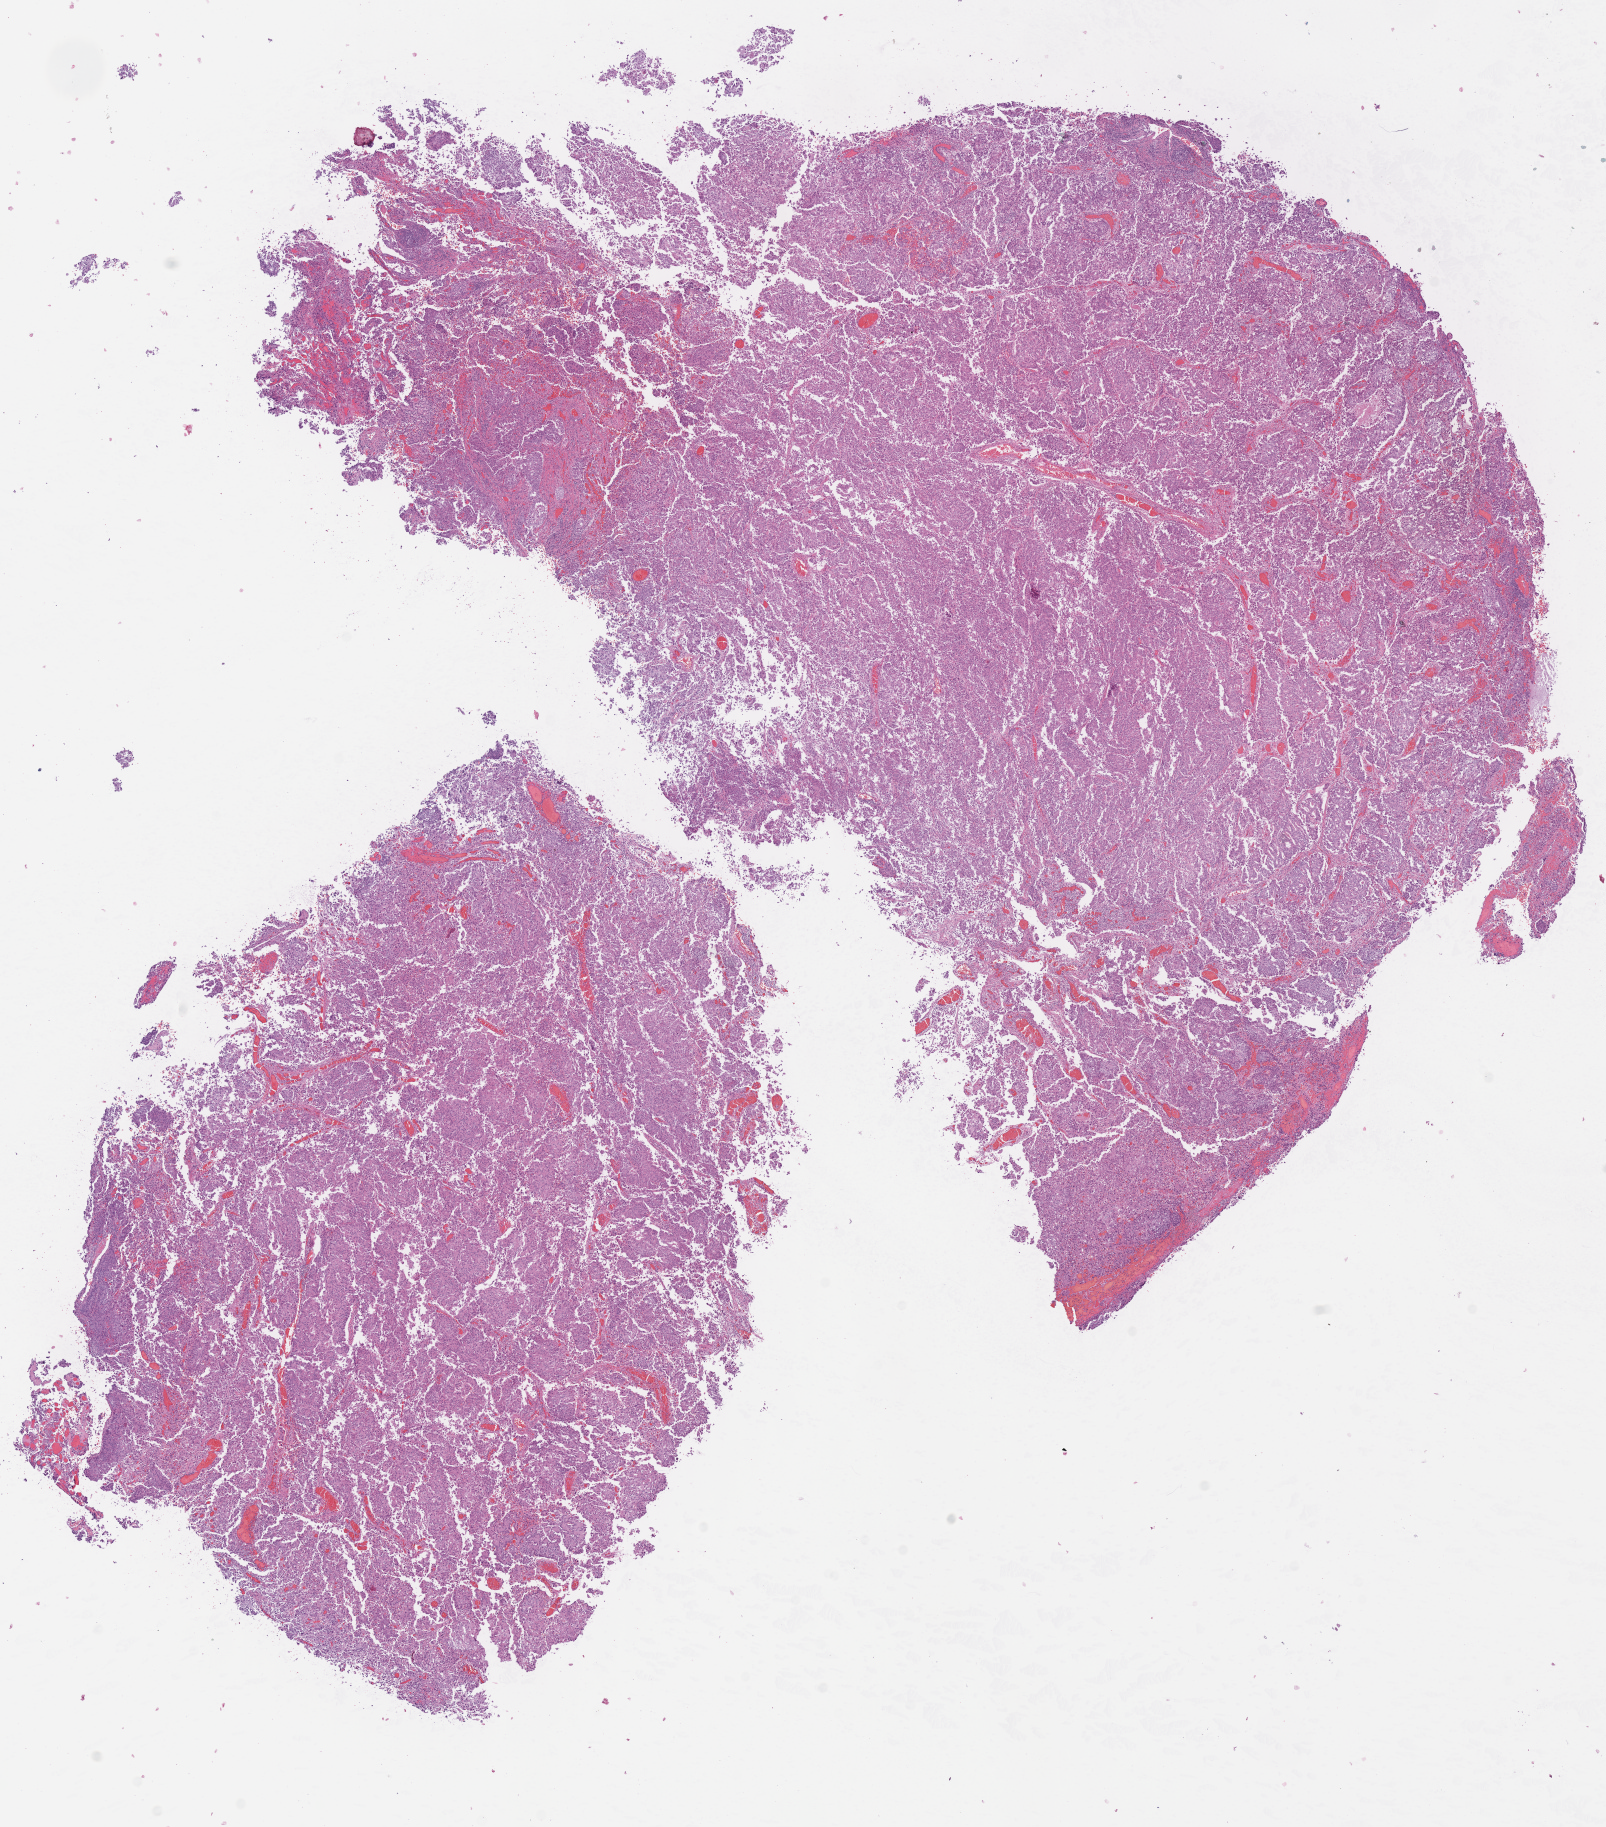
Digitized H&E-stained tissue section (whole slide) — whole scanned area (about 12.7 x 14.4 mm, acquisition: 40x scan) shown as a low-resolution overview; FFPE section; sample: primary tumour, uterus. Female patient; age at initial diagnosis 65 years. Histologic grade: G3 (poorly differentiated).
• pathologic diagnosis: Endometrioid adenocarcinoma, NOS
• FIGO stage: IA